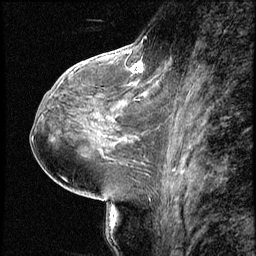
Breast MRI (dynamic contrast-enhanced), one sagittal slice; position 32 of 66 along the scan axis; 3 images stored at this slice position (order not interpretable as contrast timing); 1.5 T; TE 4.2 ms, TR 8.7 ms; 256 × 256 image matrix, field of view 180 × 180 mm. Patient: female, 38 years. From the clinical record (not read from this slice): setting: breast cancer imaged before/during neoadjuvant chemotherapy; receptor status: triple-negative.
Annotated regions visible in this slice (semi-automatic segmentation, software-assisted and operator-edited):
- analysis volume of interest (the breast-tissue region the enhancement analysis was run in; not a lesion): bounding box [x1, y1, x2, y2] px = [128, 57, 149, 78]
- tumour enhancement mask (voxels above the 140 % enhancement threshold inside the analysis volume of interest): [128, 62, 143, 73]